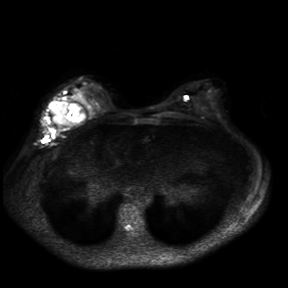
Breast MRI, one axial slice. Position 19 of 30 along the scan axis. Diffusion-weighted series; image 2 of 4 stored at this slice position (different b-values; order by instance number). 3 T. 288 × 288 image matrix, field of view 360 × 360 mm. Female patient.
Outlined on this slice (outlined manually by an expert reader):
- tumour on diffusion-weighted imaging: box from (x=49, y=100) to (x=70, y=124) px